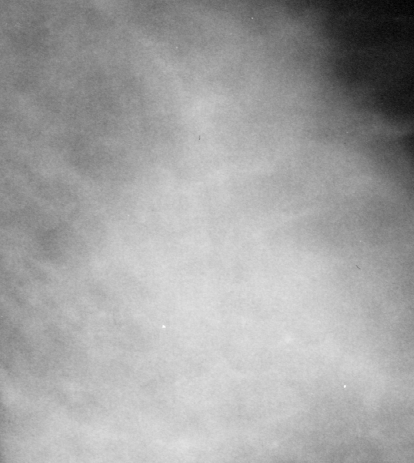
Crop from a digitized film mammogram around one marked abnormality, left breast, CC view.
- Marked abnormality: mass, shape irregular / architectural distortion, margins obscured / spiculated; BI-RADS assessment category 4; pathology (as recorded): malignant.